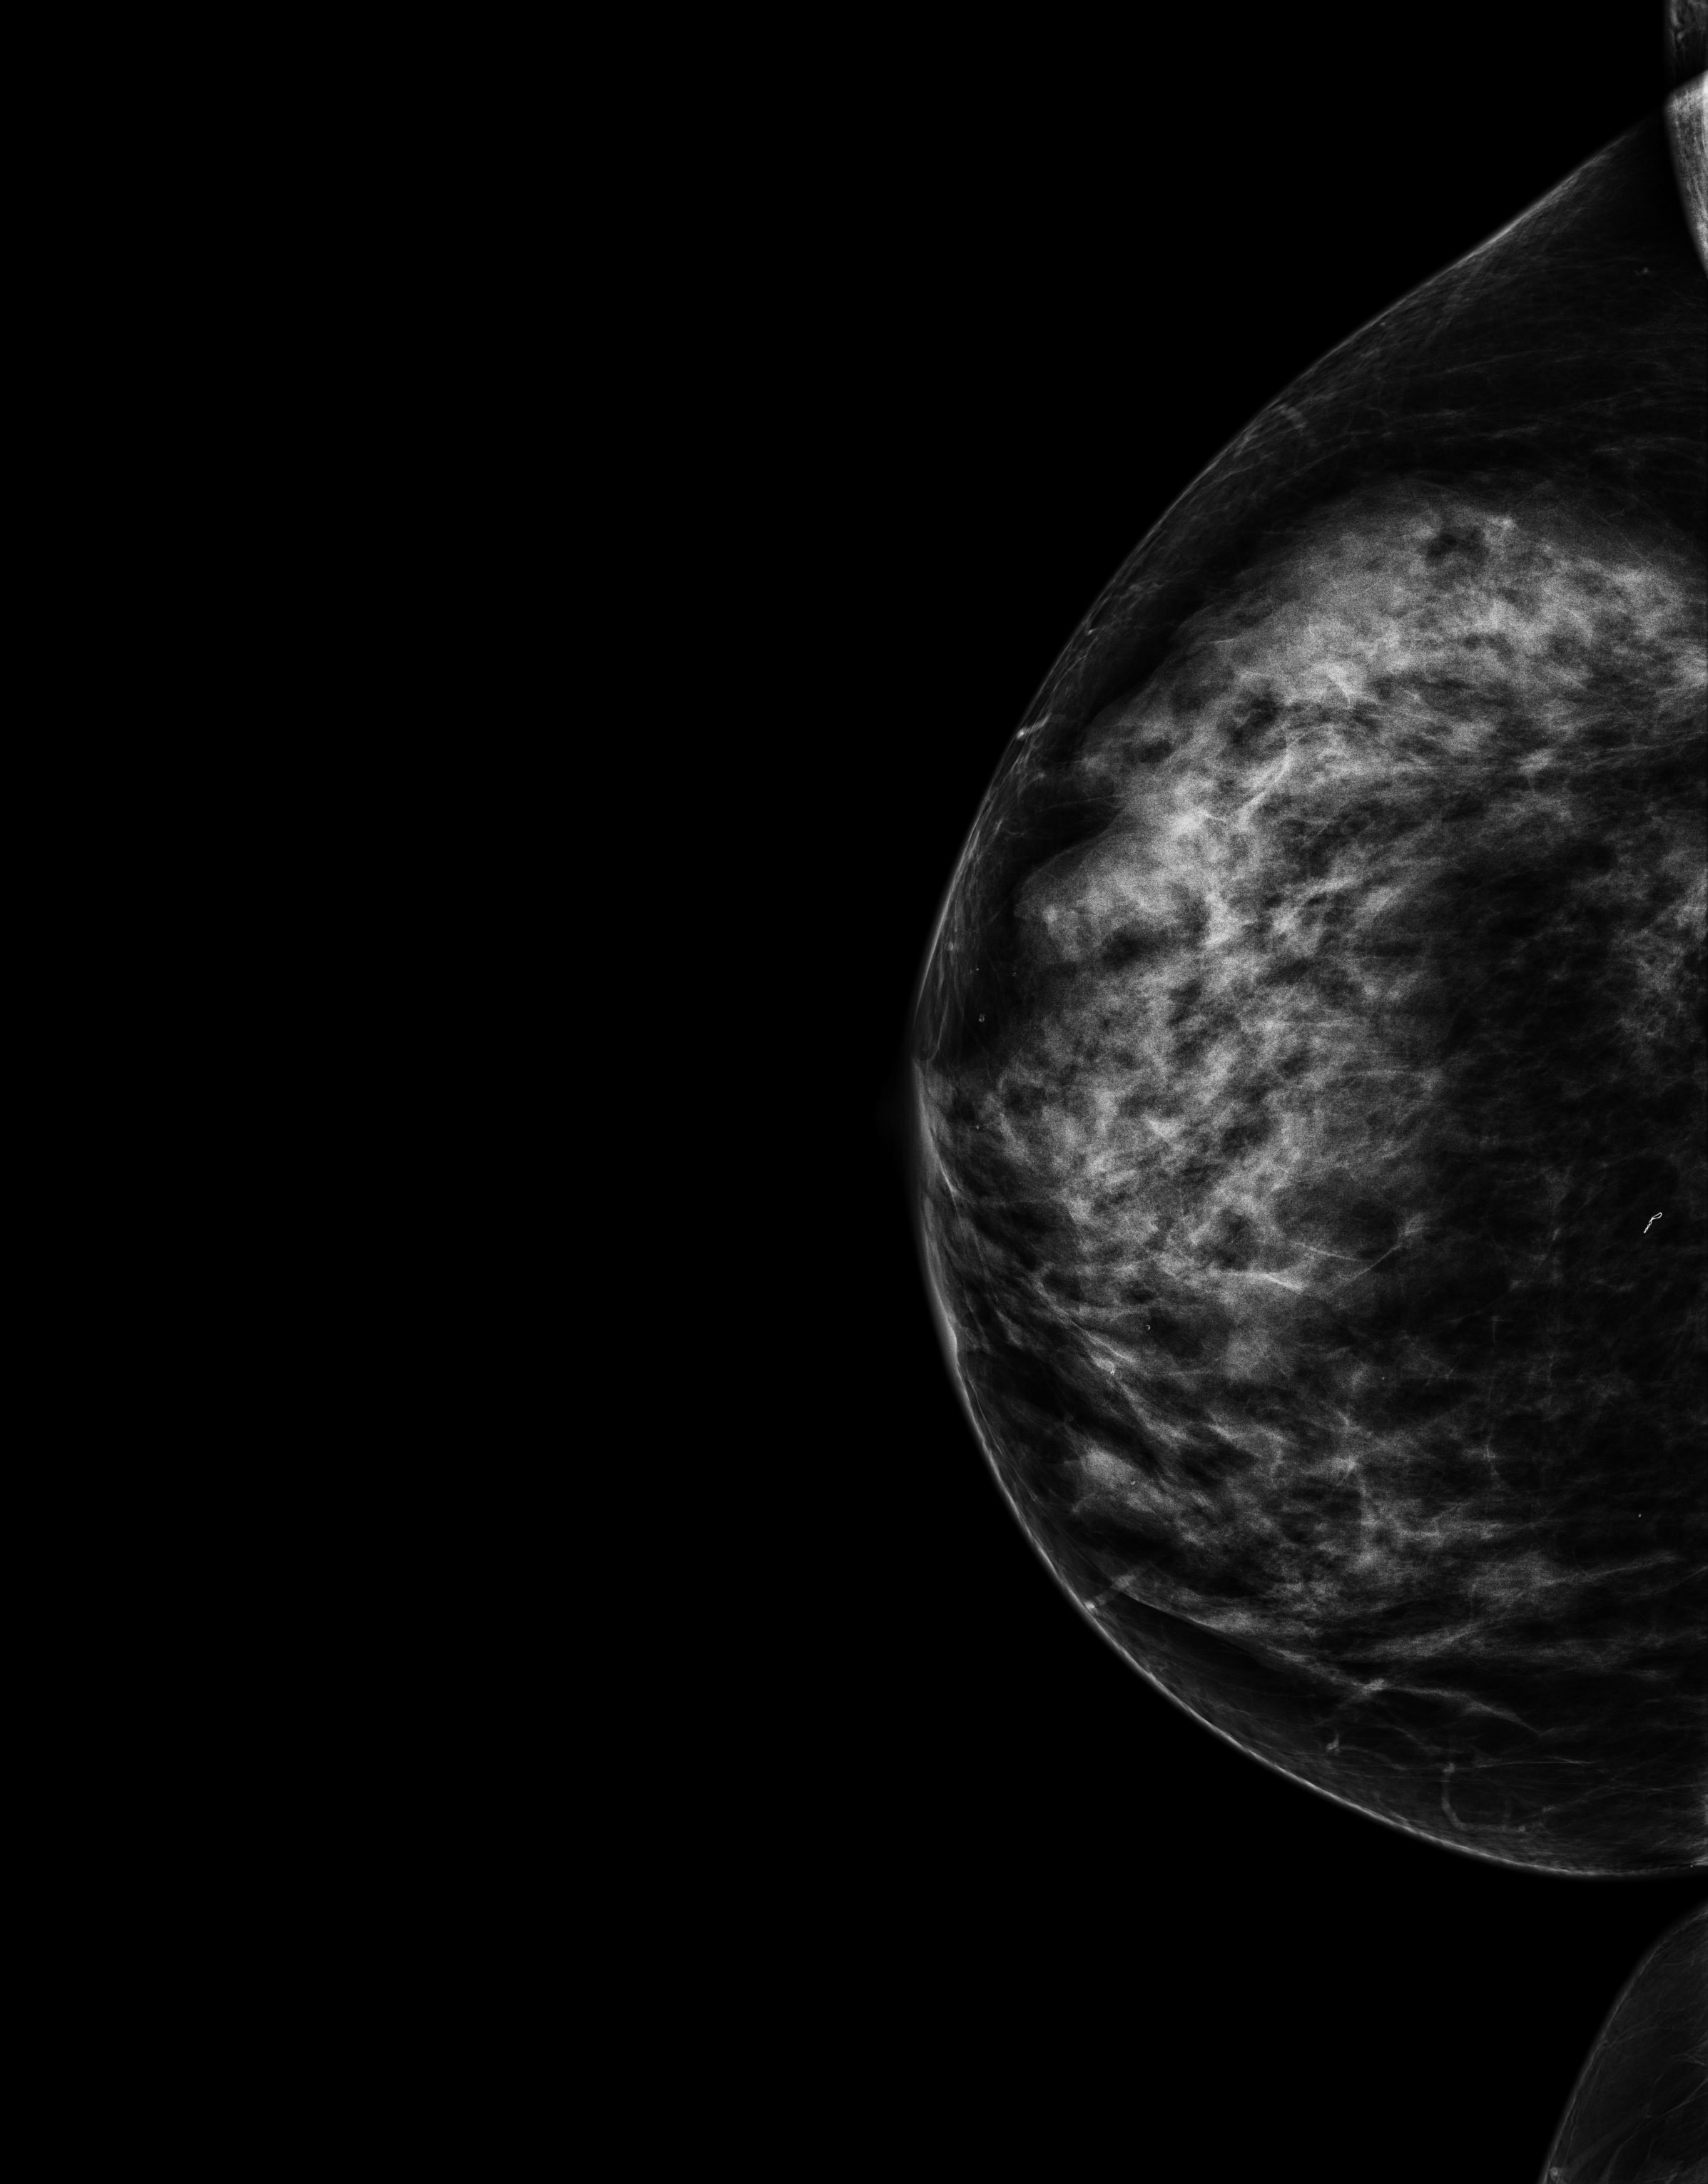
Full-field digital mammogram (FFDM); right breast; cranio-caudal projection; screening examination; system: Senographe Essential ADS_56.21.3. Patient aged 64 years (female).
- BI-RADS breast density category at the screening exam (both breasts, scale 1–4): 4
- final BI-RADS assessment for this screening round (tomosynthesis exam, both breasts): category 2
- recall: no recall after this screen